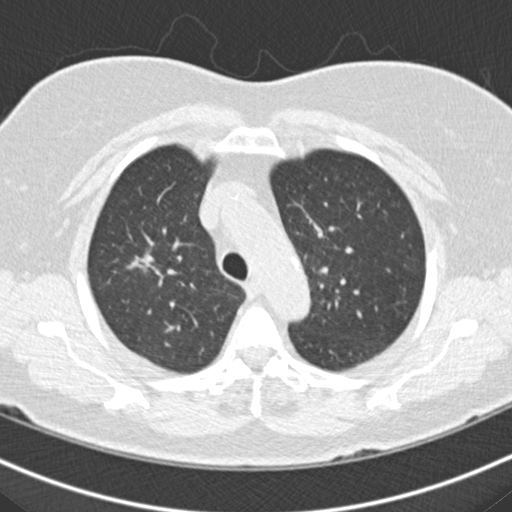
Low-dose screening chest CT, one axial slice; slice 133 of 160 in the series (ordered by position); reconstruction kernel B30f; 120 kVp; lung window (W 1500 / L -600 HU); 2 mm slice thickness; 512 × 512 image matrix, field of view 316 × 316 mm.
Outlined on this slice (manually delineated by an expert):
- lesion 3 (nodule, upper lobe of right lung): box from (x=132, y=252) to (x=153, y=272) px